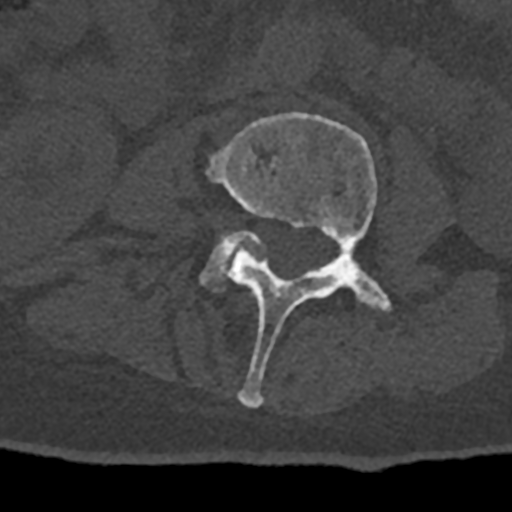
CT including the spine, one axial slice; position 310 of 797 along the scan axis; 120 kVp; bone window (W 1800 / L 400 HU); 0.5 mm slice thickness; 512 × 512 image matrix, field of view 160 × 160 mm. Male patient, age 74 years. Case-level facts recorded for this patient, not image findings: primary cancer: renal; vertebrae with lytic lesions (as recorded): T10, L1, L2, L3, L4, L5.
Annotated regions visible in this slice (semi-automatic segmentation, software-assisted and operator-edited):
- L3 vertebra: bounding box <208,112,394,408> (left, top, right, bottom; pixels)
- L4 vertebra: <202,232,265,291>